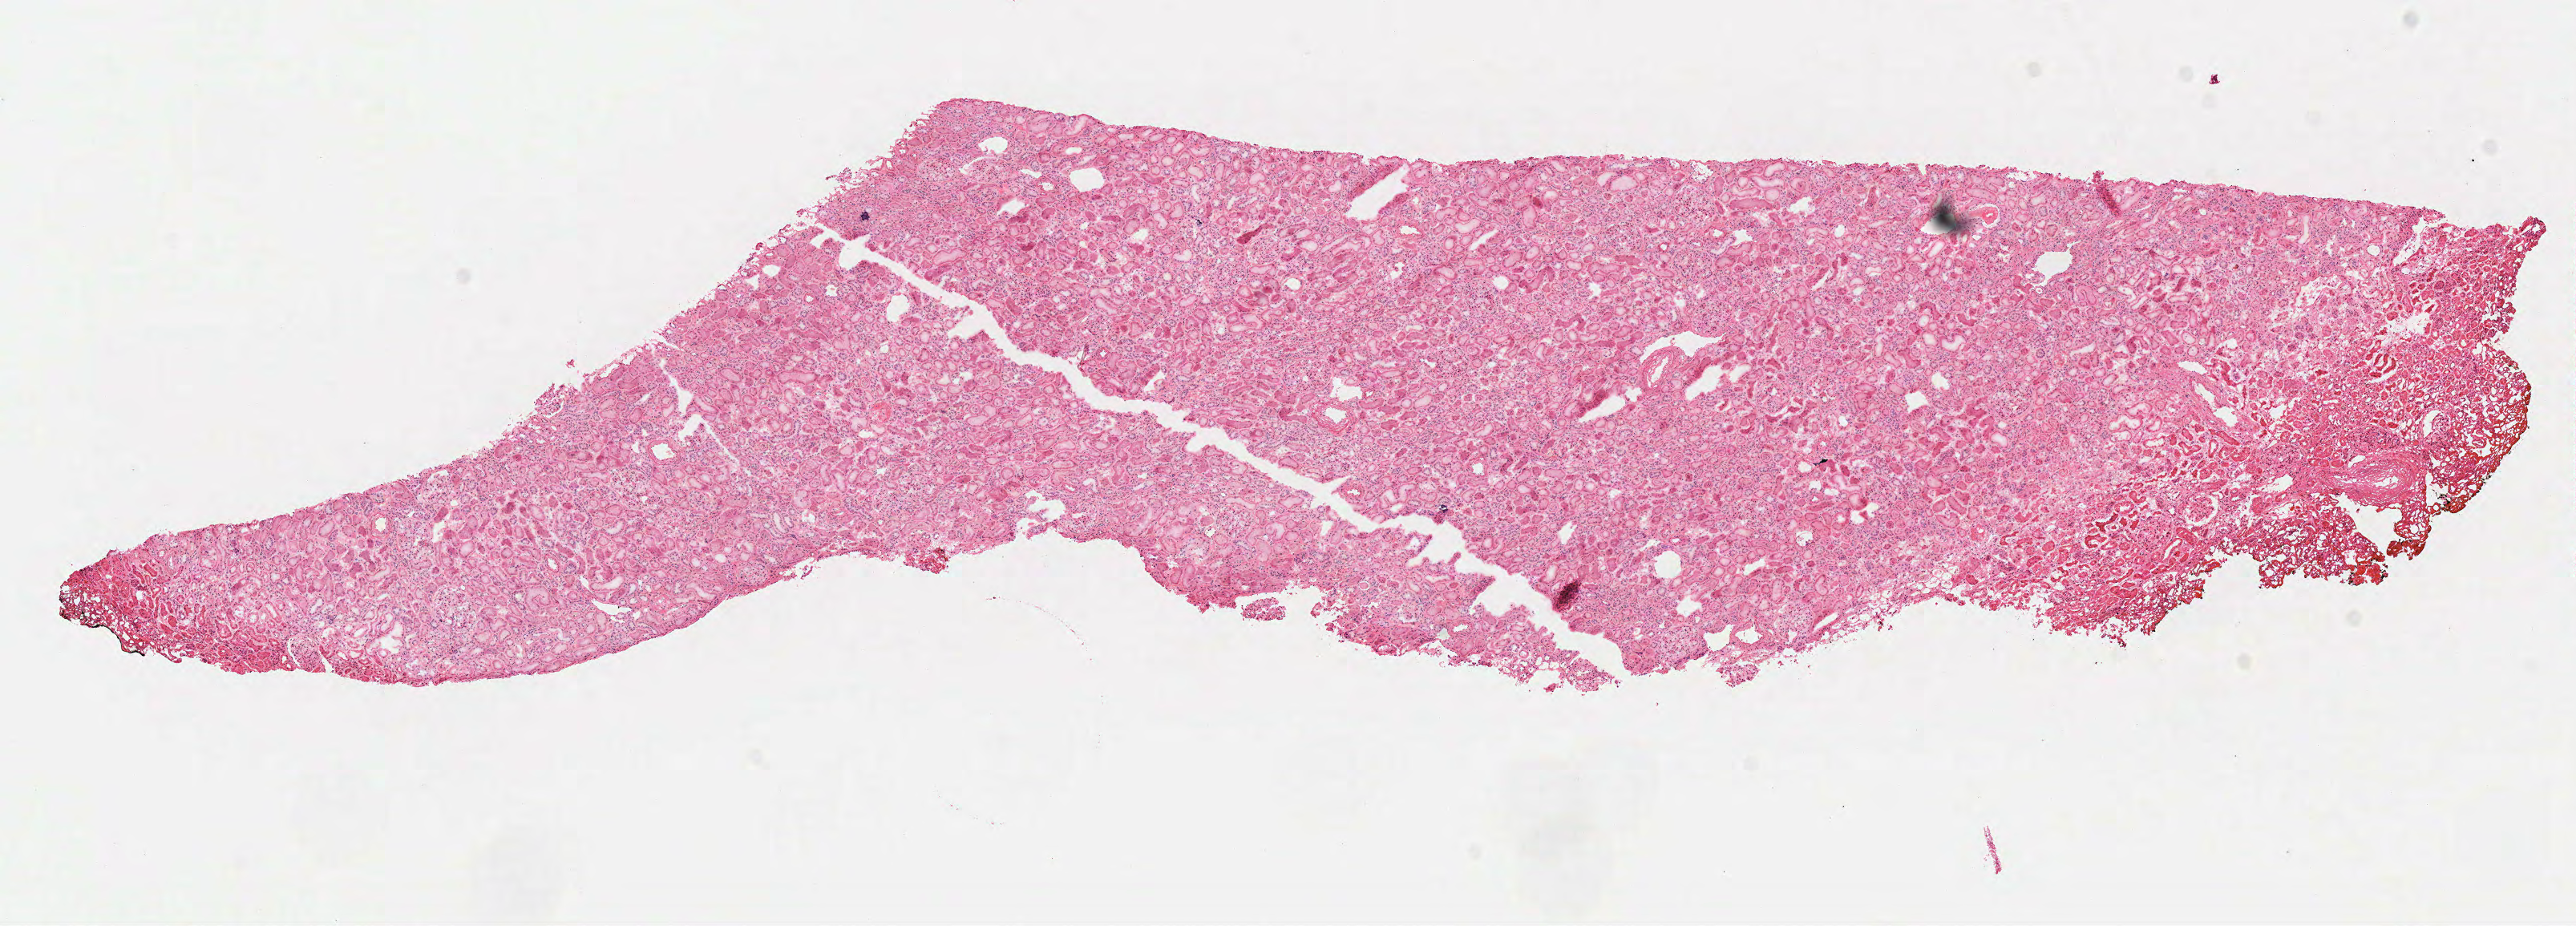
Hematoxylin and eosin (H&E) stained whole-slide image — low-resolution overview of the scanned area, about 12.7 x 4.5 mm. Frozen section from the top of the tissue portion. Sample: solid tissue normal (non-tumour tissue), kidney. Female, age 79 years at initial diagnosis.
This section: solid tissue normal sample (biorepository sample class). Patient diagnosis: Papillary adenocarcinoma, NOS.